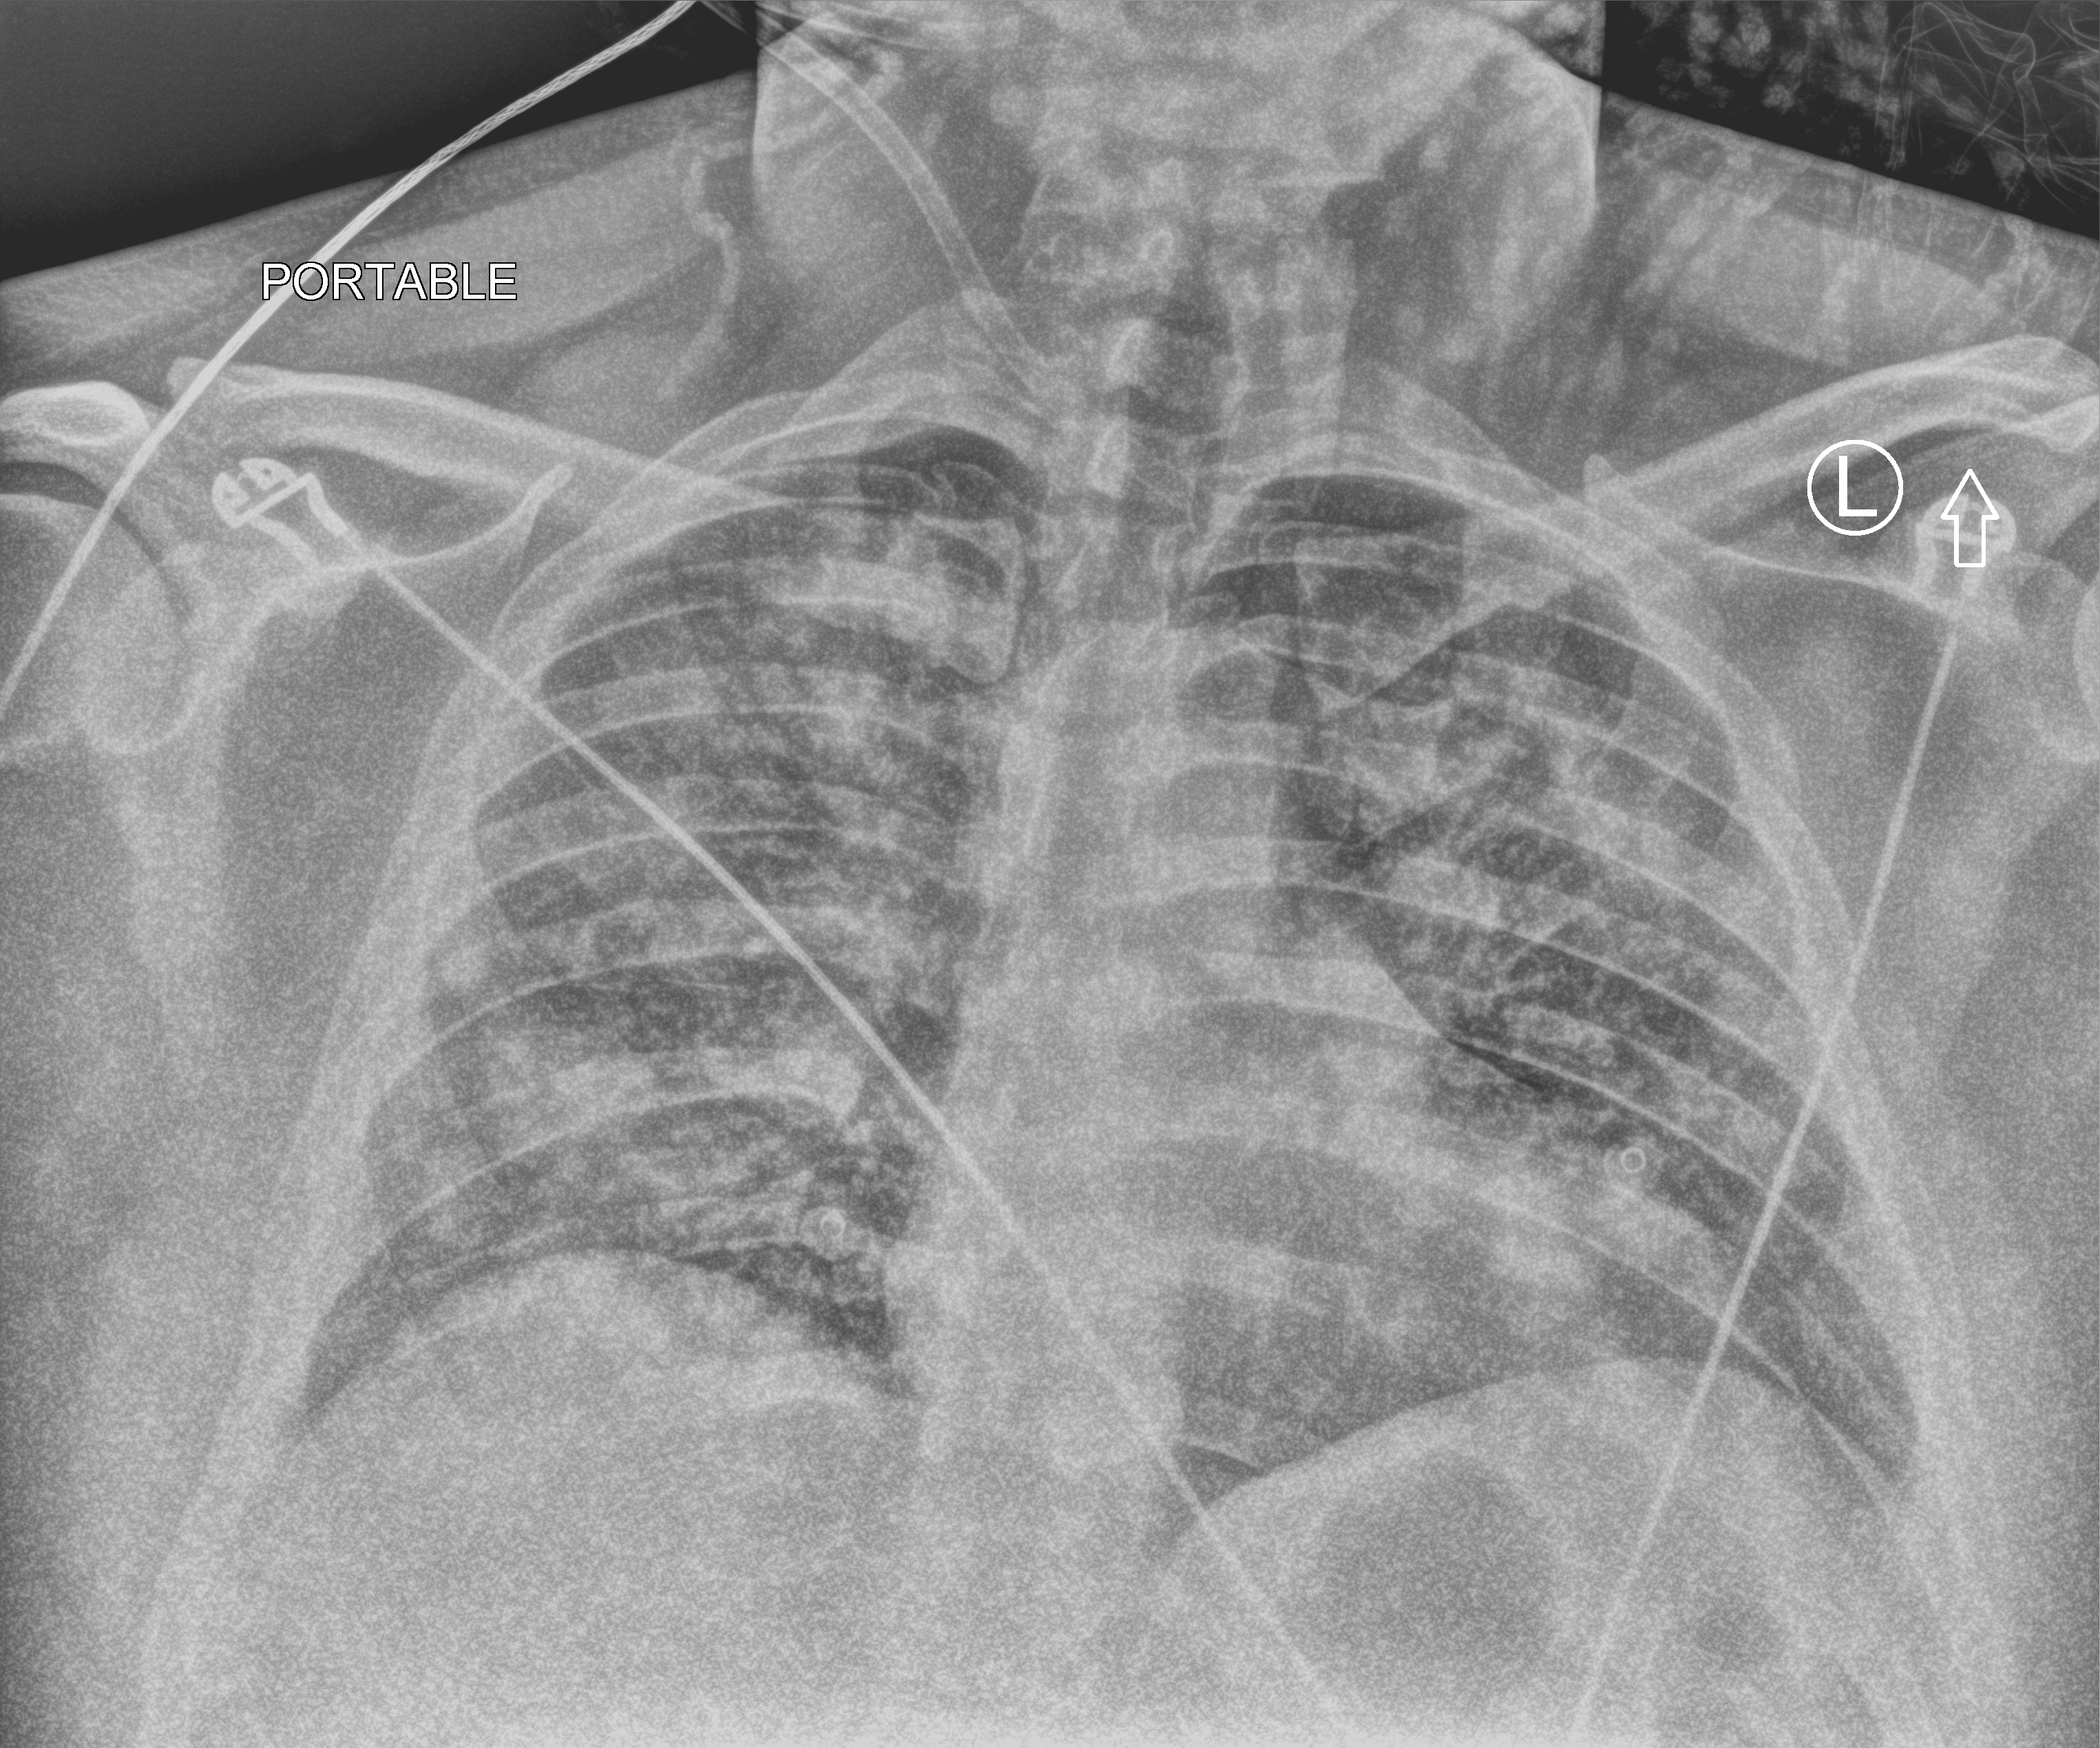
Portable chest radiograph, anteroposterior (AP) projection. Male patient hospitalised with COVID-19, age 18–59 years.
Hospital-stay facts (about this admission, not read from this image; timing relative to this image not recorded): admitted to intensive care during this hospital stay: no; length of hospital stay: 10 days.